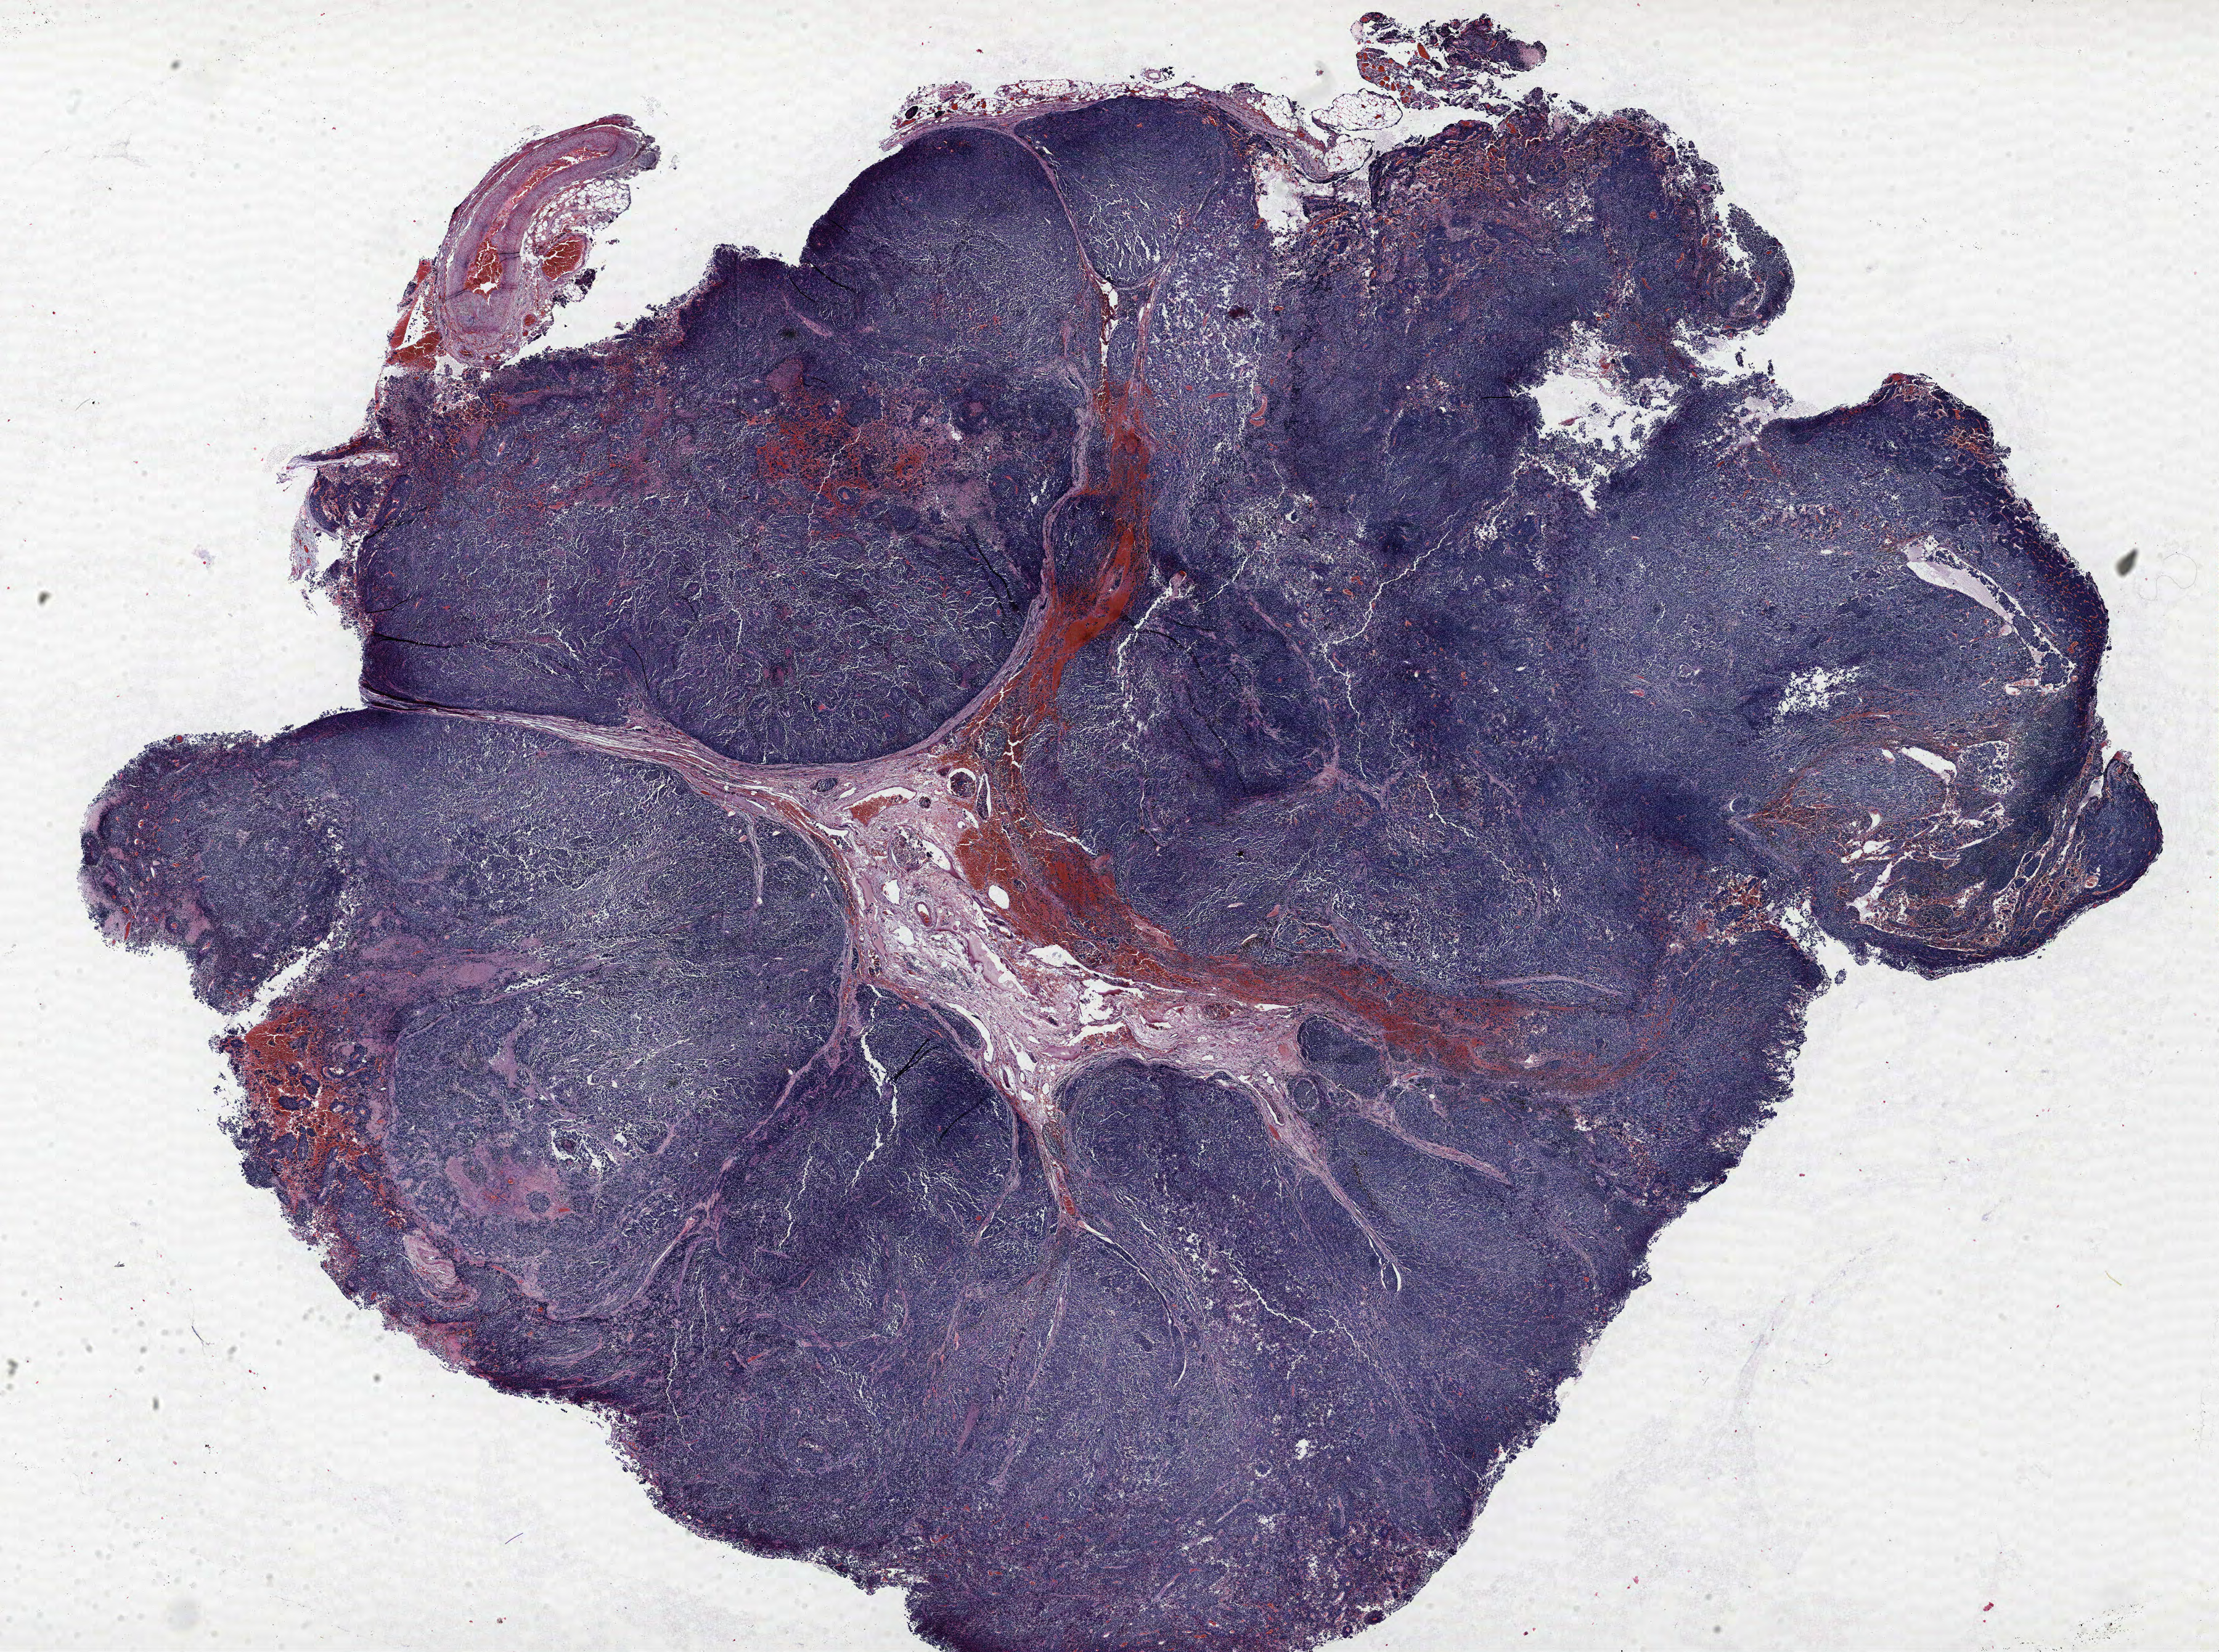
Hematoxylin and eosin (H&E) stained whole-slide image — a low-resolution overview of the entire scanned area, about 28.8 x 21.4 mm (from a 40x scan), formalin-fixed paraffin-embedded (FFPE) section, lung tissue. Male, age 68 at enrolment. Current smoker at enrolment. Grade: undifferentiated (G4).
Stage (AJCC 6th edition): IIIB. Tumour size (pathology): 30 mm. Primary tumour location (clinical record): right upper lobe. Participant's lung-cancer diagnosis: Combined small cell carcinoma (ICD-O-3 8045/3).